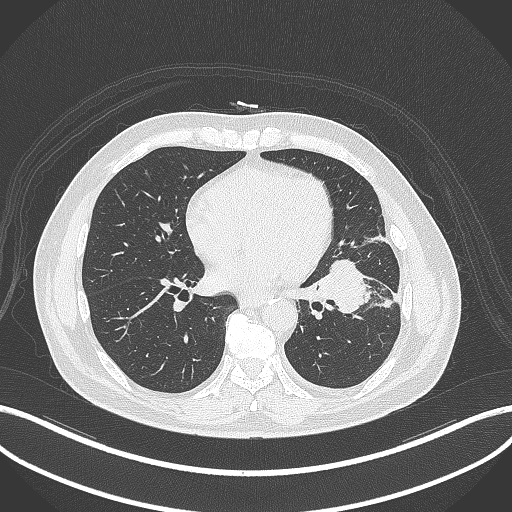
Chest CT, one axial slice; slice 152 of 230 in the series (ordered by position); reconstruction kernel B70f; lung window (W 1500 / L -600 HU); 1 mm slice thickness; 512 × 512 image matrix, field of view 400 × 400 mm. Male patient, age 68 years. From the clinical record (not read from this slice): clinical TNM (as recorded): T2b N0 M0.
Structures marked on this image (rectangle marked by the reading radiologist):
- lung tumour (recorded histology: squamous cell carcinoma): box from (x=313, y=256) to (x=373, y=321) px